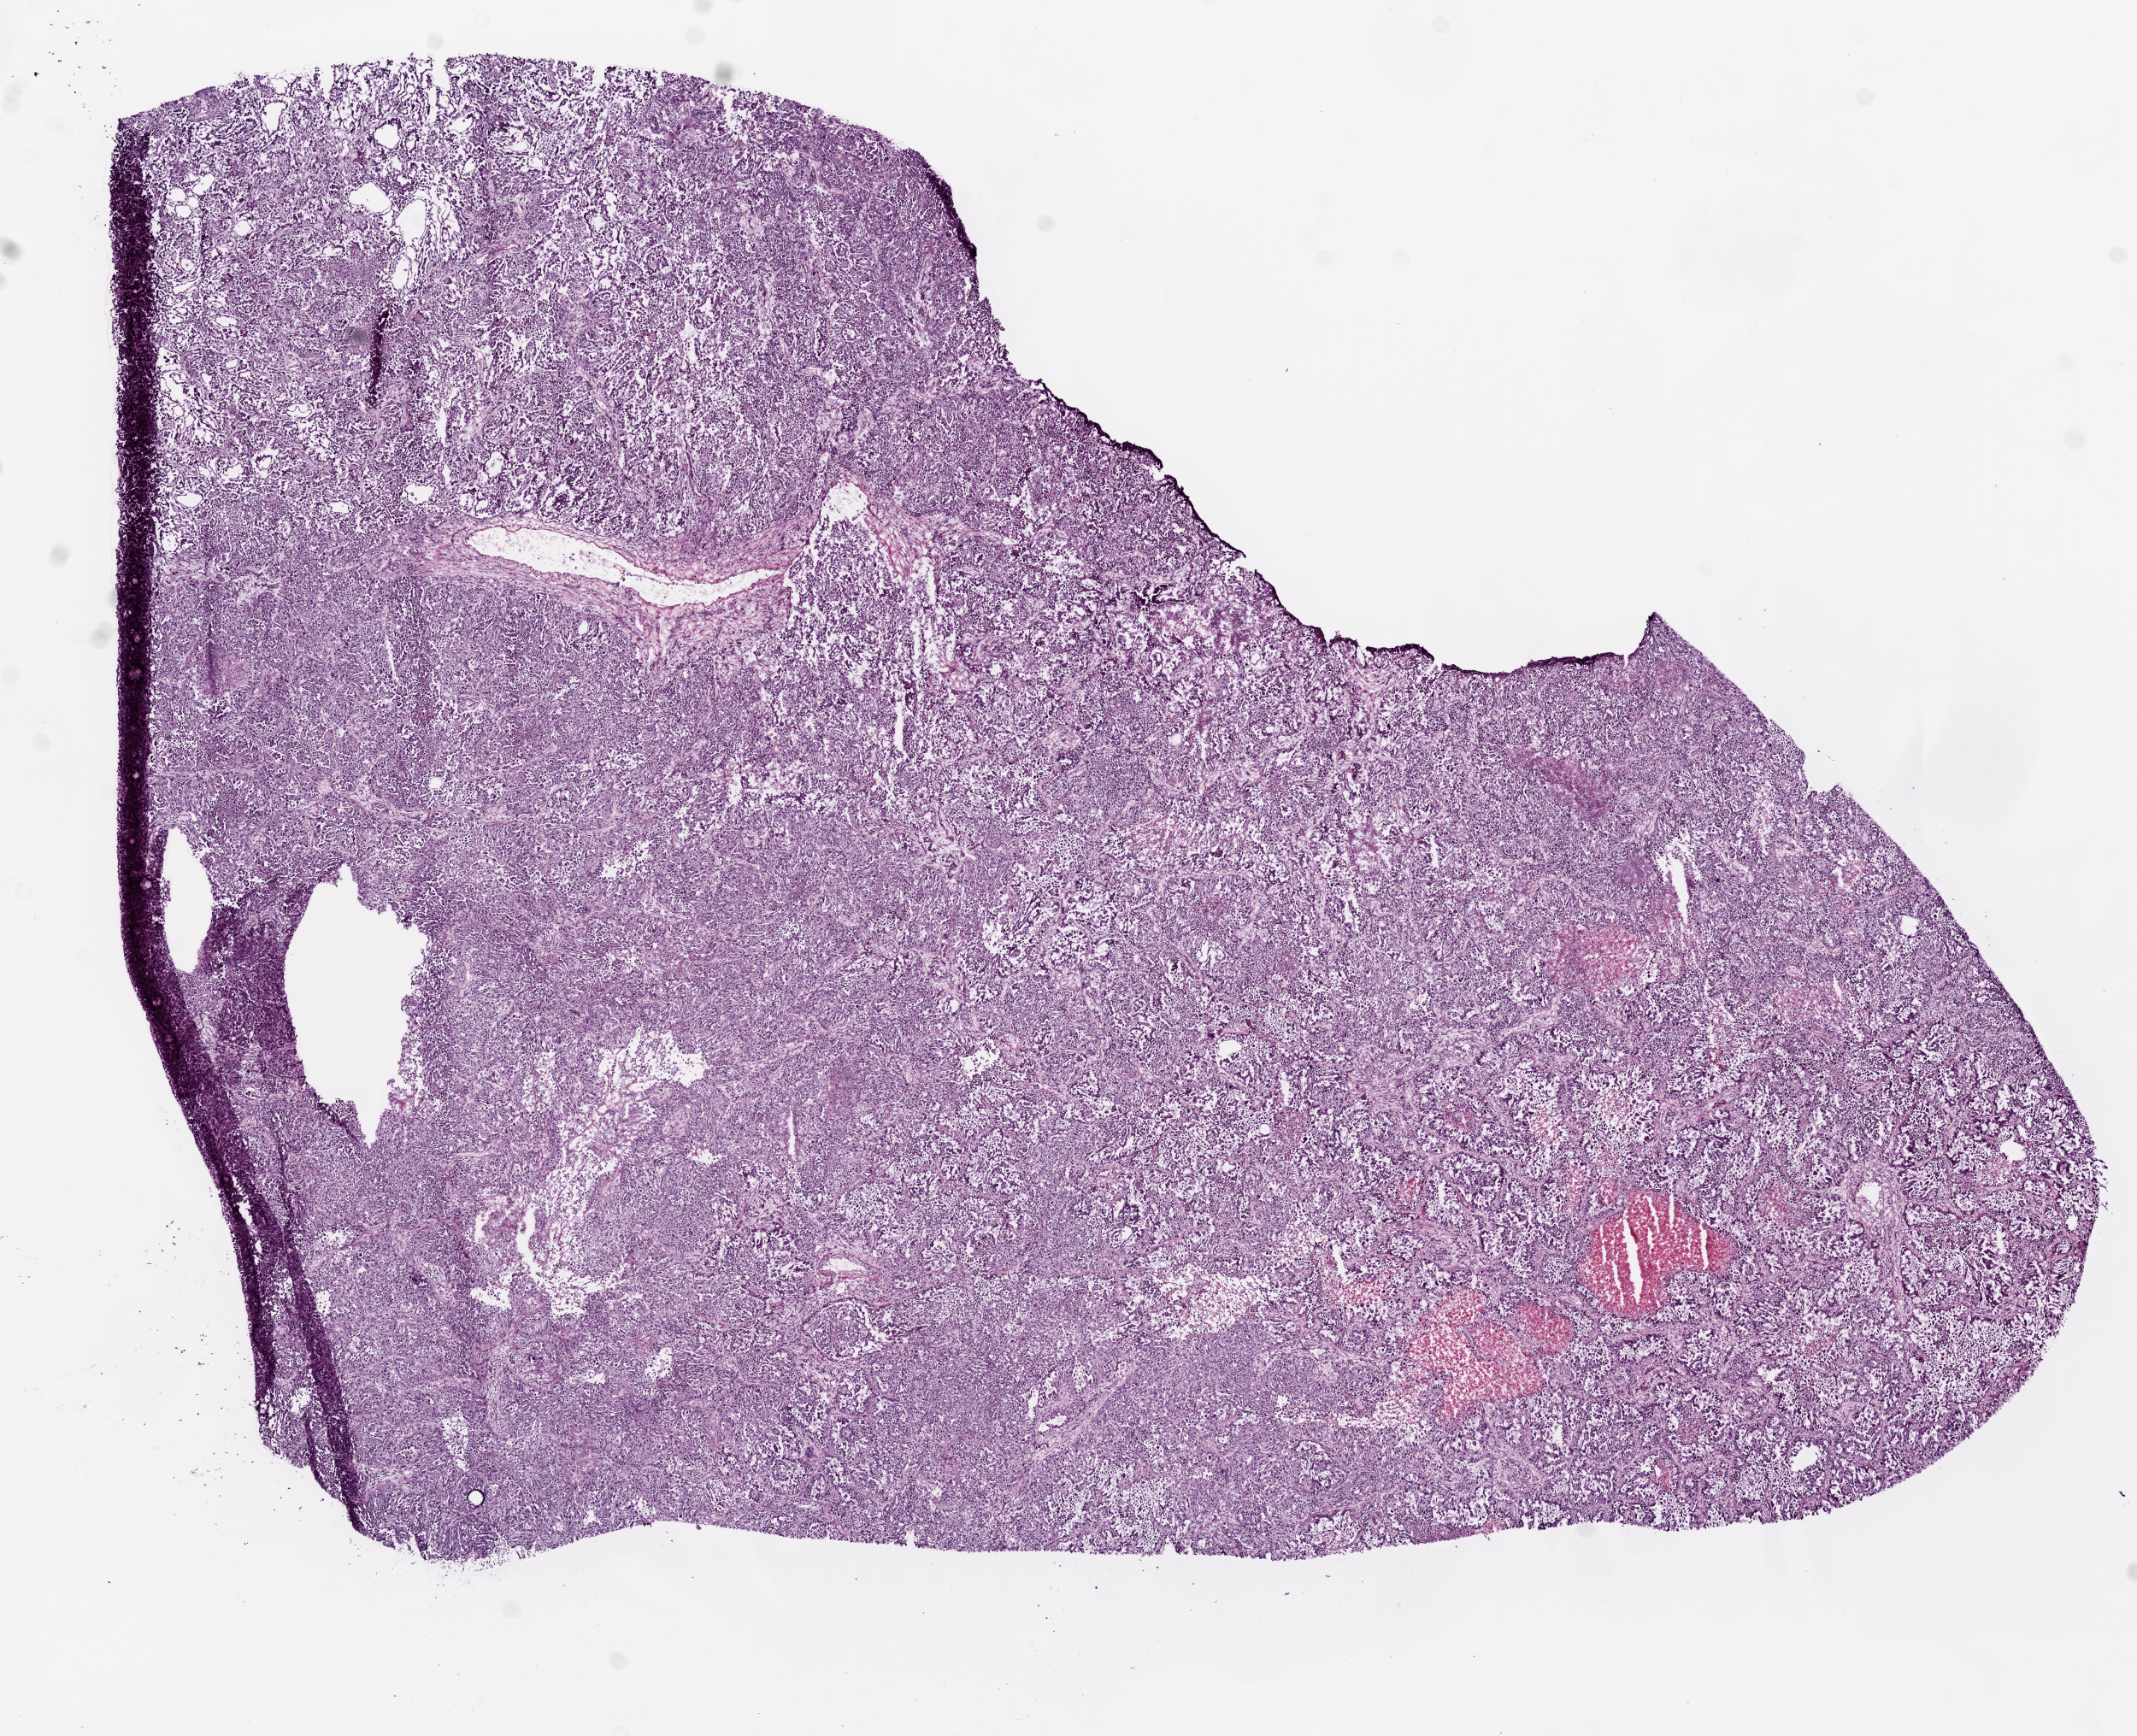
Whole-slide histology image, Hematoxylin and eosin (H&E) stained — a low-resolution overview of the entire scanned area, about 10.0 x 8.1 mm (from a 20x scan). Frozen section from the top of the tissue portion. Lung, primary tumour sample. Male patient; age at initial diagnosis 71 years. Slide review estimates, as recorded: tumour cells 90%, tumour nuclei 75%, normal cells 0%, stromal cells 10%, necrosis 5%.
Histologic diagnosis: Adenocarcinoma with mixed subtypes. AJCC pathologic stage: IB (6th edition).